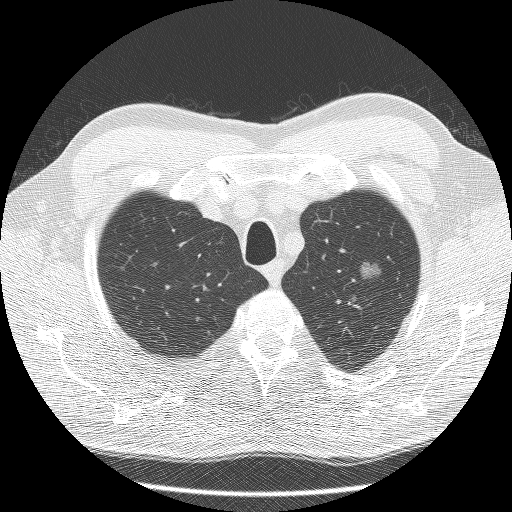
Low-dose screening chest CT, axial slice, third screening round (two years after baseline), lung window (W 1500 / L -600 HU), lung (sharp) reconstruction kernel (BONE), 120 kVp, slice 19 of 132 in the series, 512 × 512 image matrix, field of view 340 × 340 mm. Male participant, aged 60 years at enrolment.
Expert-annotated lung lesion, bounding box <335,251,392,300> (left, top, right, bottom; pixels). The screening reader recorded 2 non-calcified nodules or masses ≥4 mm on this exam (right lower lobe, left upper lobe); which of them this box marks is not recorded. Official screen result: positive, other. Later outcome: lung cancer diagnosed 99 days after this screen — bronchiolo-alveolar carcinoma, non-mucinous, left upper lobe, well differentiated (G1), stage IA (AJCC 6th edition), 16 mm at pathology.